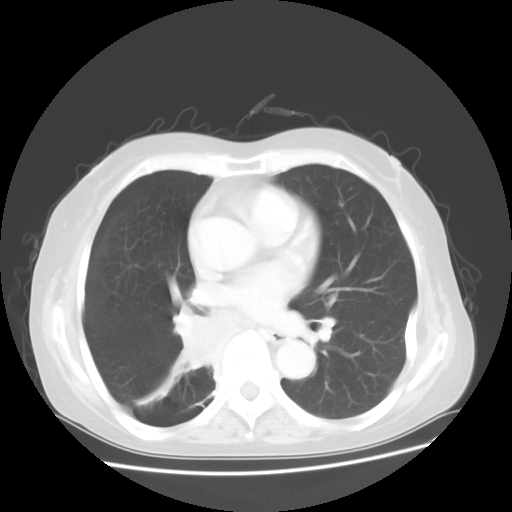
Chest CT, one axial slice; position 23 of 48 along the scan axis; lung window (W 1500 / L -600 HU); 5 mm slice thickness; 512 × 512 image matrix, field of view 360 × 360 mm. Female patient, age 63 years. Case-level facts recorded for this patient, not image findings: clinical TNM (as recorded): T2 N3 M1b; histopathological grade: G3.
Structures marked on this image (rectangle marked by the reading radiologist):
- lung tumour (recorded histology: small cell carcinoma): bounding box <176,311,220,376> (left, top, right, bottom; pixels)